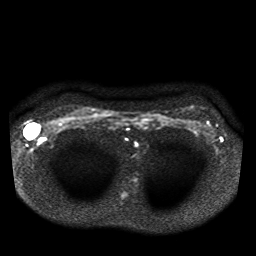
Breast MRI, one axial slice. Diffusion-weighted series; image 2 of 4 stored at this slice position (different b-values; order by instance number). 1.5 T. 5 mm slice thickness. 256 × 256 image matrix, field of view 330 × 330 mm. Female patient.
Structures marked on this image (manually delineated by an expert):
- tumour on diffusion-weighted imaging: bounding box [x1, y1, x2, y2] px = [25, 124, 36, 139]